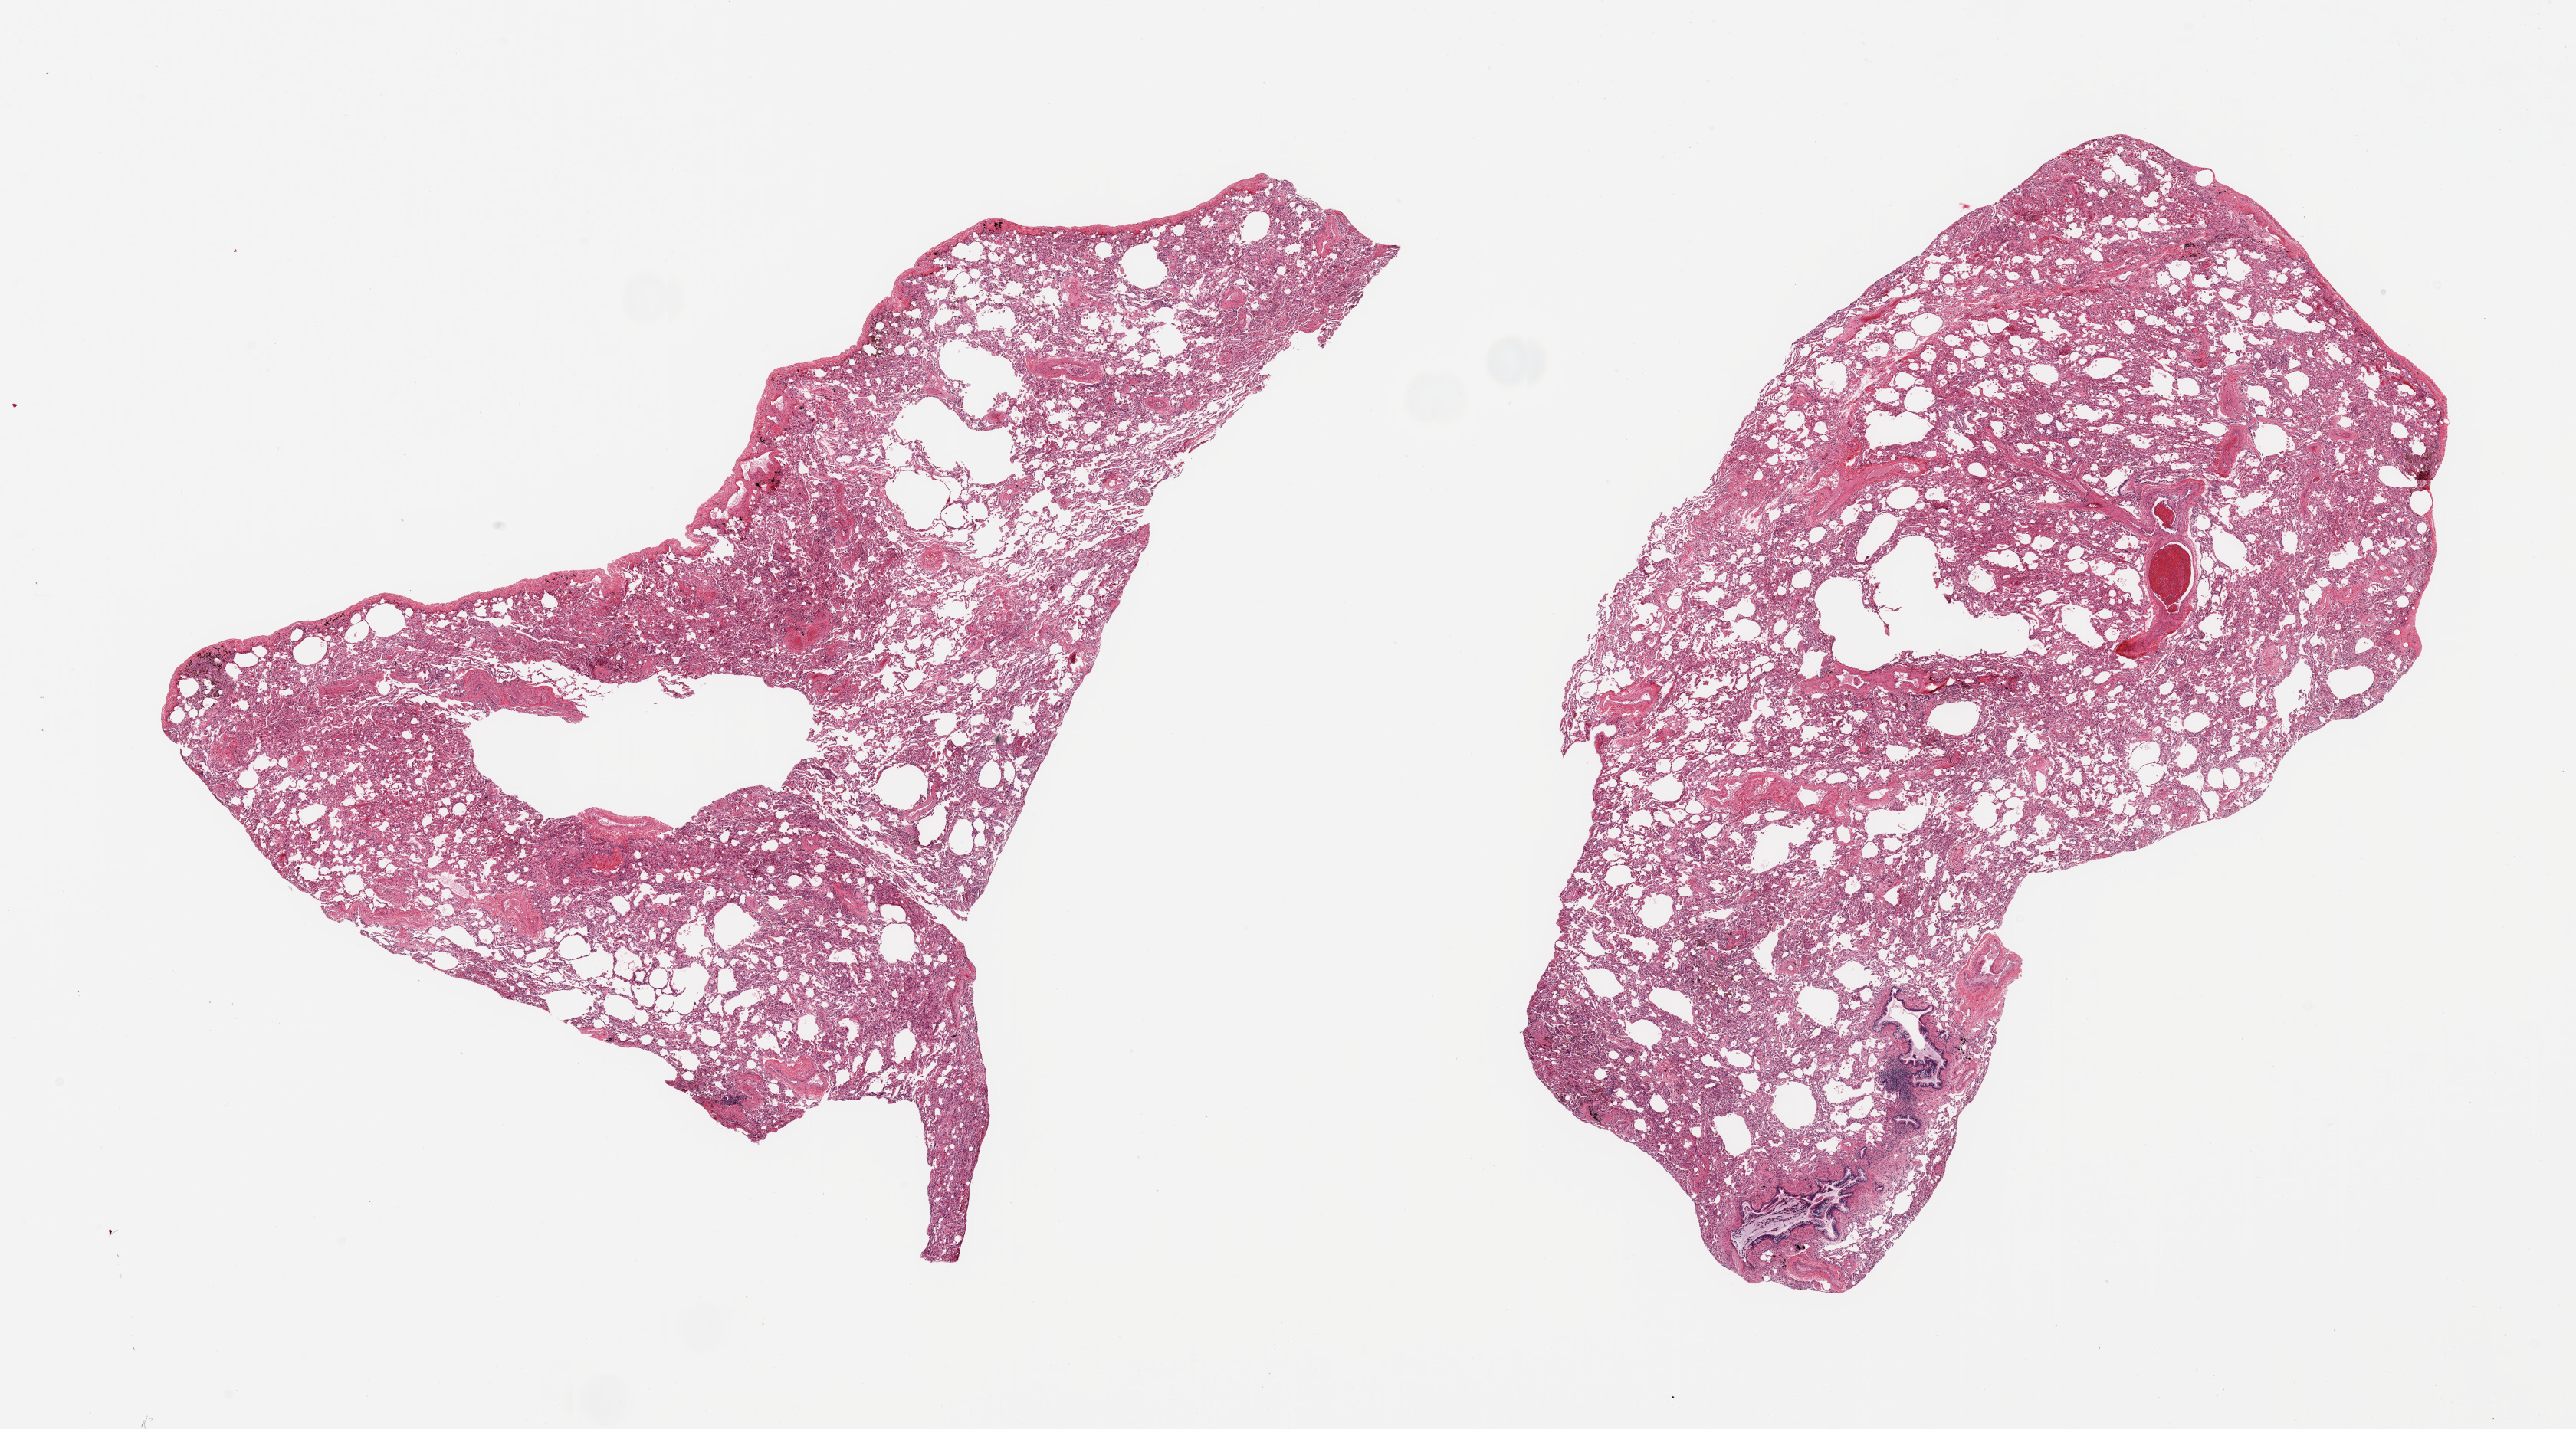
Hematoxylin and eosin (H&E) whole-slide image, brightfield, whole scanned area (about 26.6 x 14.7 mm) shown as a low-resolution overview; PAXgene-fixed paraffin-embedded (PFPE) section; section of lung (target tissue); tissue donor sample. Donor: female.
Reviewer comment on this tissue sample: 2 pieces; moderate emphysema.